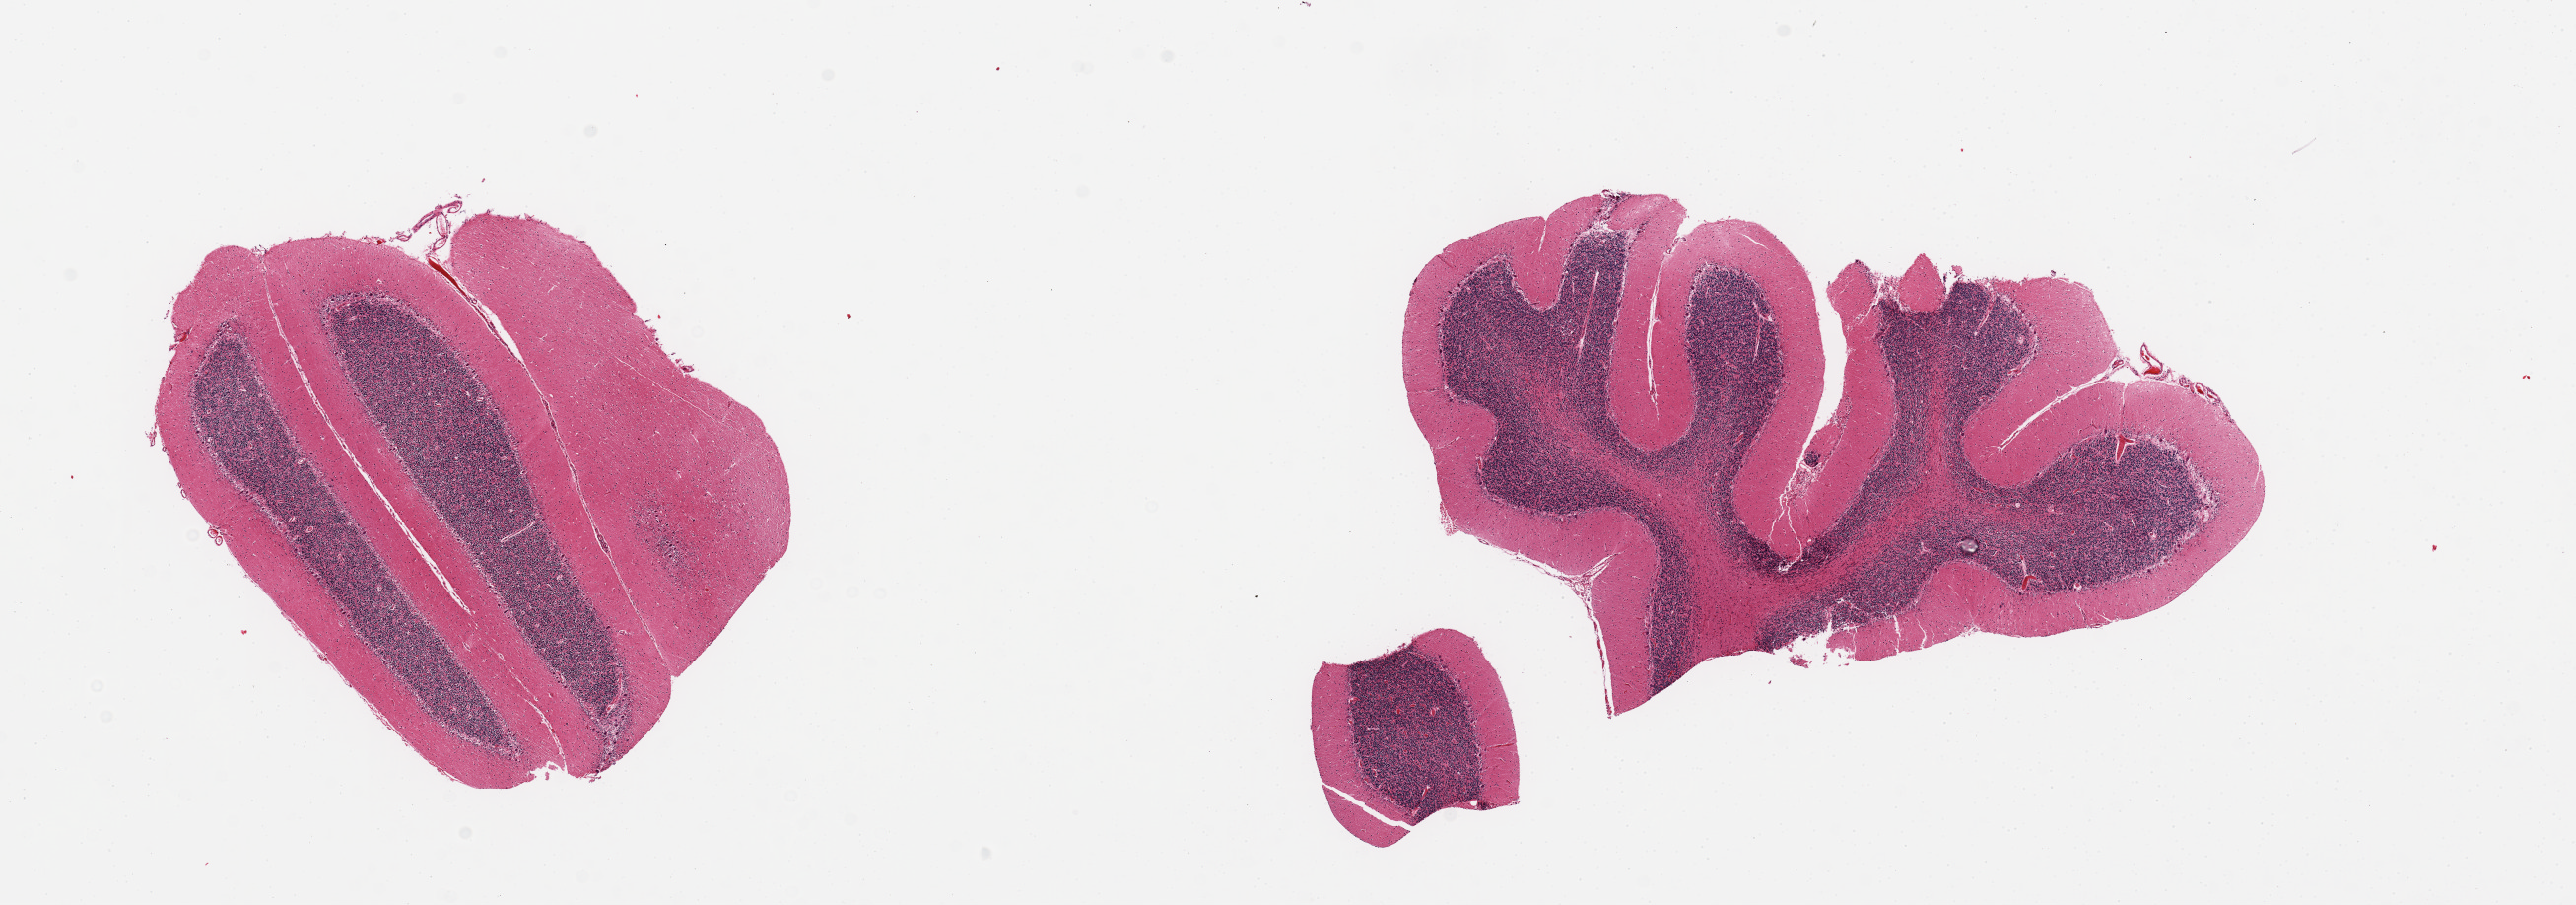
Digitized H&E-stained section, brightfield, whole scanned area (about 20.7 x 7.3 mm, from a 20x scan) shown as a low-resolution overview; PAXgene-fixed, paraffin-embedded tissue; sampled site (target tissue): cerebellum; donor tissue sample.
- reviewer comment on this tissue sample: 2 pieces, no abnormalities